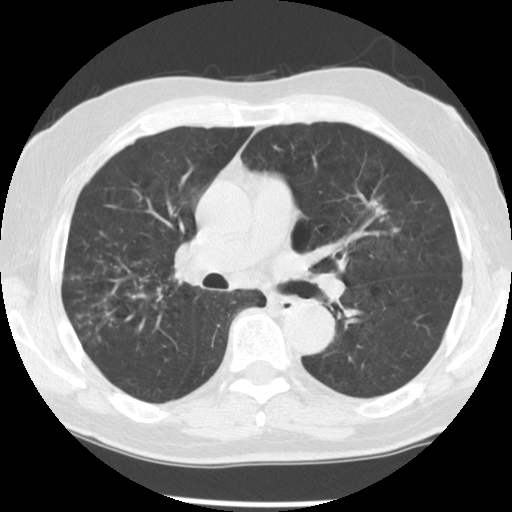
Low-dose screening chest CT, one axial slice; slice 74 of 131 in the series (ordered by position); reconstruction kernel STANDARD; lung window (W 1500 / L -600 HU); 2.5 mm slice thickness; 512 × 512 image matrix.
Annotated regions visible in this slice (outlined manually by an expert reader):
- lesion 1 (tumor, upper lobe of left lung): bounding box (x1, y1, x2, y2) in pixels: (374, 204, 386, 217)